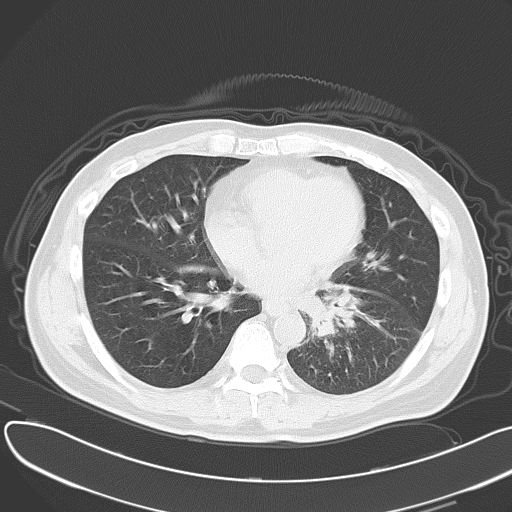
Chest CT, one axial slice. Position 22 of 55 along the scan axis. Reconstruction kernel B70f. 120 kVp. Lung window (W 1500 / L -600 HU). 5 mm slice thickness. 512 × 512 image matrix. Male patient, age 55 years. Case-level facts recorded for this patient, not image findings: clinical TNM (as recorded): T2 N3 M0.
Annotated regions visible in this slice (rectangle marked by the reading radiologist):
- lung tumour (recorded histology: small cell carcinoma): bounding box [x1, y1, x2, y2] px = [299, 292, 362, 351]